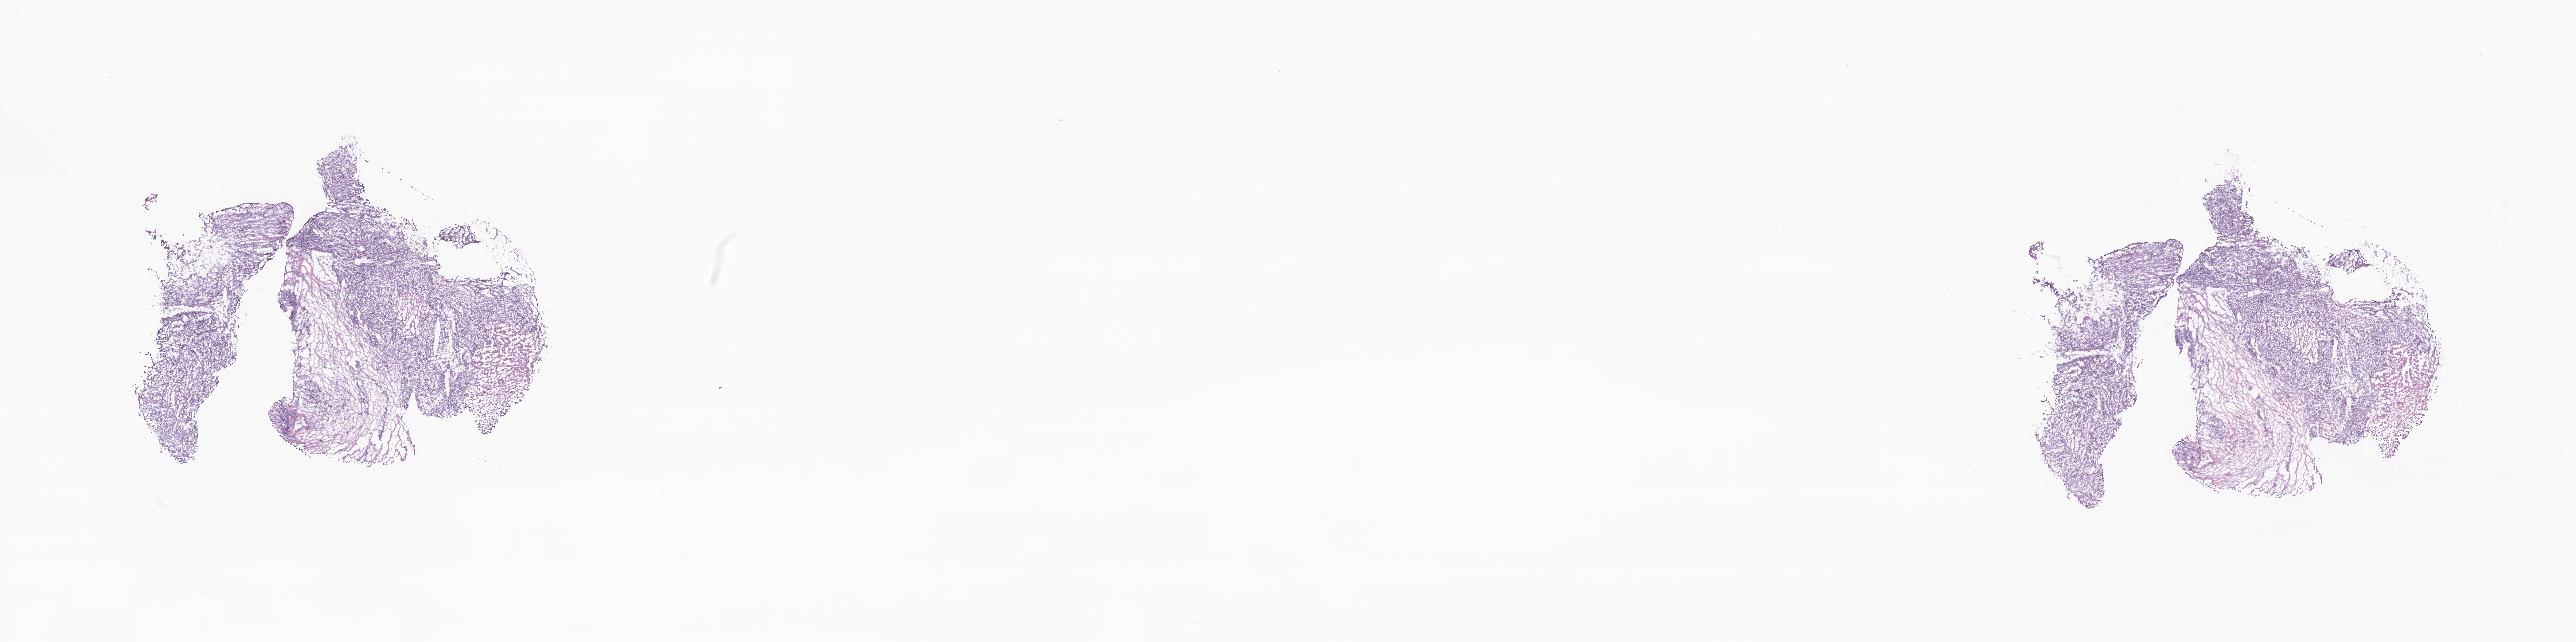
H&E whole-slide image, low-resolution overview of the scanned area, about 35.4 x 8.8 mm; frozen section; metastatic tumor tissue, resected from lymph nodes of axilla or arm. Female patient; age at initial diagnosis 74 years. Pathologist review of this section (percent, as recorded): tumor cells 70%, tumor nuclei 75%, stromal cells 0%, necrosis 10%, normal cells 20%. Infiltration values recorded for this section: lymphocyte infiltration 0%, monocyte infiltration 0%, neutrophil infiltration 0%.
Patient diagnosis (primary): Infiltrating duct carcinoma, NOS. Section: bottom of the tissue portion.